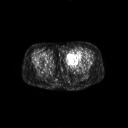
FDG PET of an extremity soft-tissue mass (from a PET/CT study), one axial slice; slice 22 of 267 in the series (ordered by position); 128 × 128 image matrix. Patient: female, 47 years. Case-level facts recorded for this patient, not image findings: histological type: myxofibrosarcoma; grade: intermediate; site of the primary tumour: left thigh.
Structures marked on this image (expert contour drawn on MRI and transferred to this co-registered scan by the dataset authors):
- gross tumour volume including surrounding oedema: box from (x=66, y=51) to (x=82, y=65) px
- gross tumour volume (mass): (x=66, y=52)–(x=82, y=64)